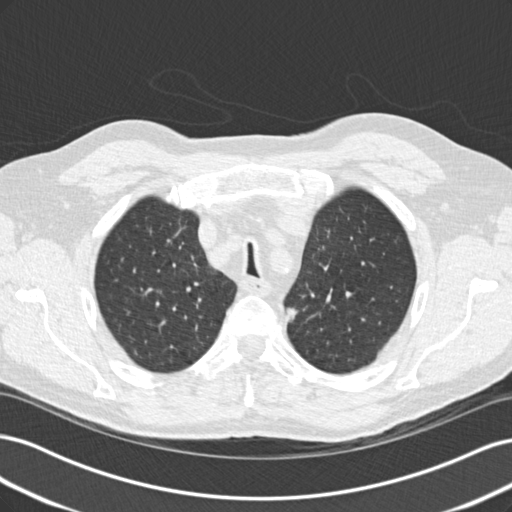
Chest CT (low-dose screening protocol), one axial image; baseline annual screen; lung window (W 1500 / L -600 HU); 2 mm slice thickness; standard (soft-tissue) reconstruction kernel (B30f); slice 38 of 206 in the series. Male participant, aged 70 years at enrolment. Current smoker at enrolment.
- Expert-annotated lung lesion, bounding box [x1, y1, x2, y2] px = [268, 295, 309, 336].
- The screening reader recorded 3 non-calcified nodules or masses ≥4 mm on this exam; which of them this box marks is not recorded.
- Participant outcome: lung cancer diagnosed 889 days after this screen (after the third annual screen) — mixed cell adenocarcinoma, left upper lobe, poorly differentiated (G3), stage IIB (AJCC 6th edition), 17 mm at pathology.